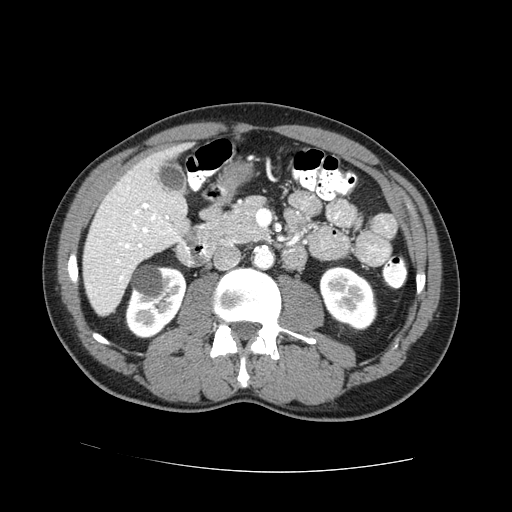
Contrast-enhanced abdominal CT (liver protocol), one axial slice; slice 22 of 73 in the series (ordered by position); one of 2 acquisitions stored at this slice position; soft-tissue window (W 400 / L 40 HU); 2.5 mm slice thickness; 512 × 512 image matrix, field of view 380 × 380 mm. From the clinical record (not read from this slice): diagnosis: hepatocellular carcinoma (patient treated with transarterial chemoembolisation; whether this scan precedes or follows treatment is not stated here); TNM stage (as recorded): Stage-IVA; Child-Pugh class: A; tumour differentiation: no biopsy.
Structures marked on this image (semi-automatically segmented with operator editing):
- liver parenchyma outside the tumour (the mass and vessels are separate outlines, so this box may not span the whole liver): bounding box (x1, y1, x2, y2) in pixels: (82, 142, 190, 316)
- liver vessels: (116, 203, 171, 281)